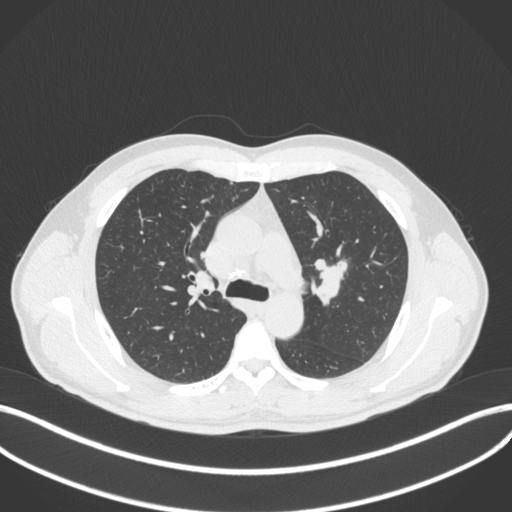
Chest CT, one axial slice. Slice 281 of 383 in the series (ordered by position). Lung window (W 1500 / L -600 HU). 1 mm slice thickness. 512 × 512 image matrix, field of view 400 × 400 mm. Male patient, age 50 years. From the clinical record (not read from this slice): clinical TNM (as recorded): T1c N1 M1b.
Outlined on this slice (rectangle marked by the reading radiologist):
- lung tumour (recorded histology: squamous cell carcinoma): box from (x=311, y=253) to (x=347, y=307) px